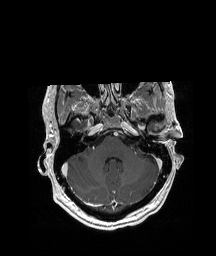
Brain MRI from a brain-tumour surgery series, one axial slice; T1-weighted post-contrast; 216 × 256 image matrix, field of view 228 × 270 mm. Case-level facts recorded for this patient, not image findings: histopathology: Glioblastoma; WHO grade: 4; IDH mutation: no.
Outlined on this slice (manually delineated by an expert):
- tumour: bounding box [x1, y1, x2, y2] px = [133, 117, 139, 121]